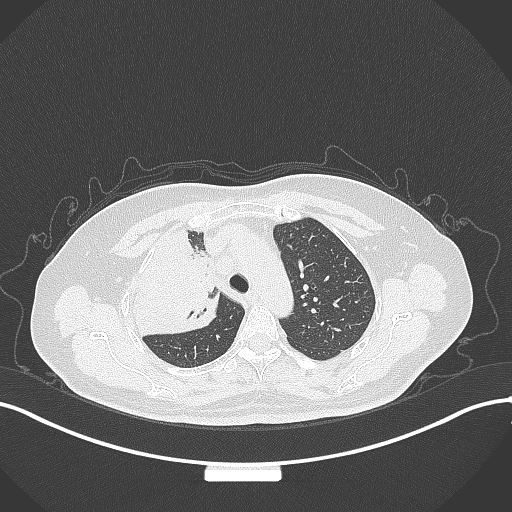
Chest CT, one axial slice; position 235 of 309 along the scan axis; lung window (W 1500 / L -600 HU); 512 × 512 image matrix, field of view 400 × 400 mm. Female patient, age 60 years. From the clinical record (not read from this slice): clinical TNM (as recorded): T3 N1 M1.
Outlined on this slice (rectangle marked by the reading radiologist):
- lung tumour (recorded histology: adenocarcinoma): box from (x=129, y=225) to (x=227, y=337) px